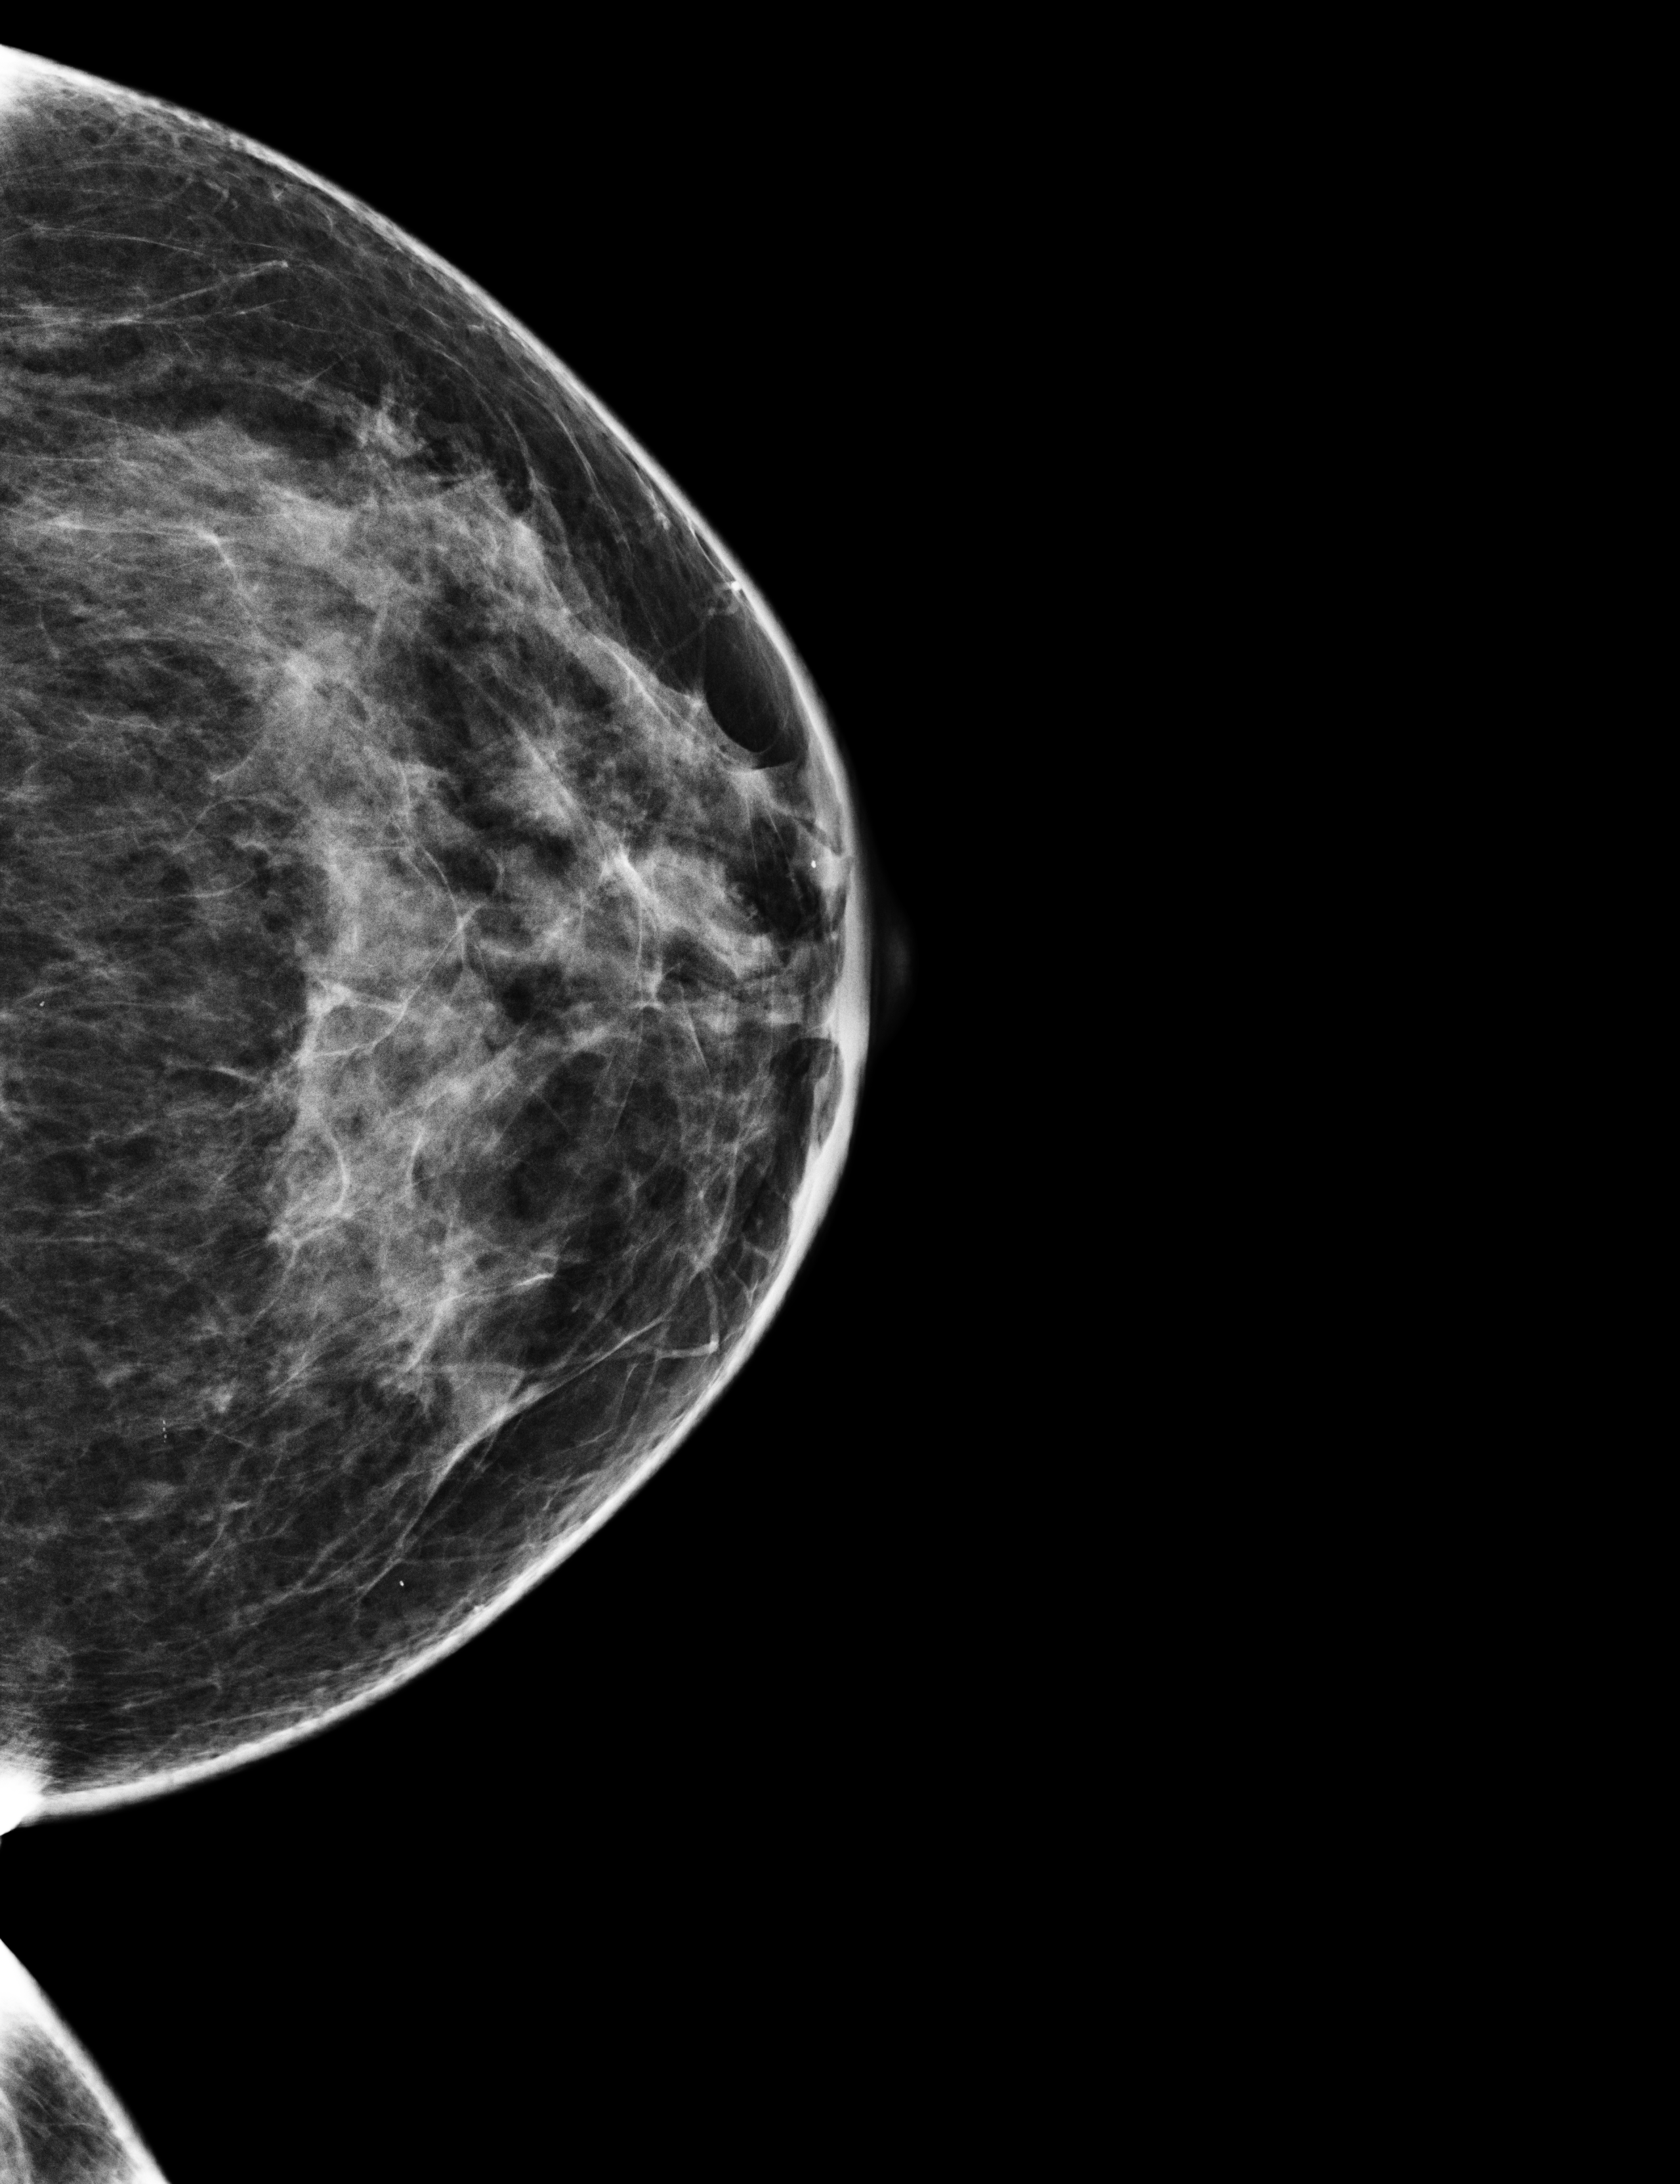
Digital mammogram (FFDM), left breast, craniocaudal (CC) view, annual screening mammography examination, compressed breast thickness 50 mm. Patient aged 46 years (female).
- breast density at the screening exam (both breasts): heterogeneously dense (BI-RADS density category c)
- final BI-RADS category for the screening round (tomosynthesis exam, both breasts): category 2
- recall: no recall after this screen